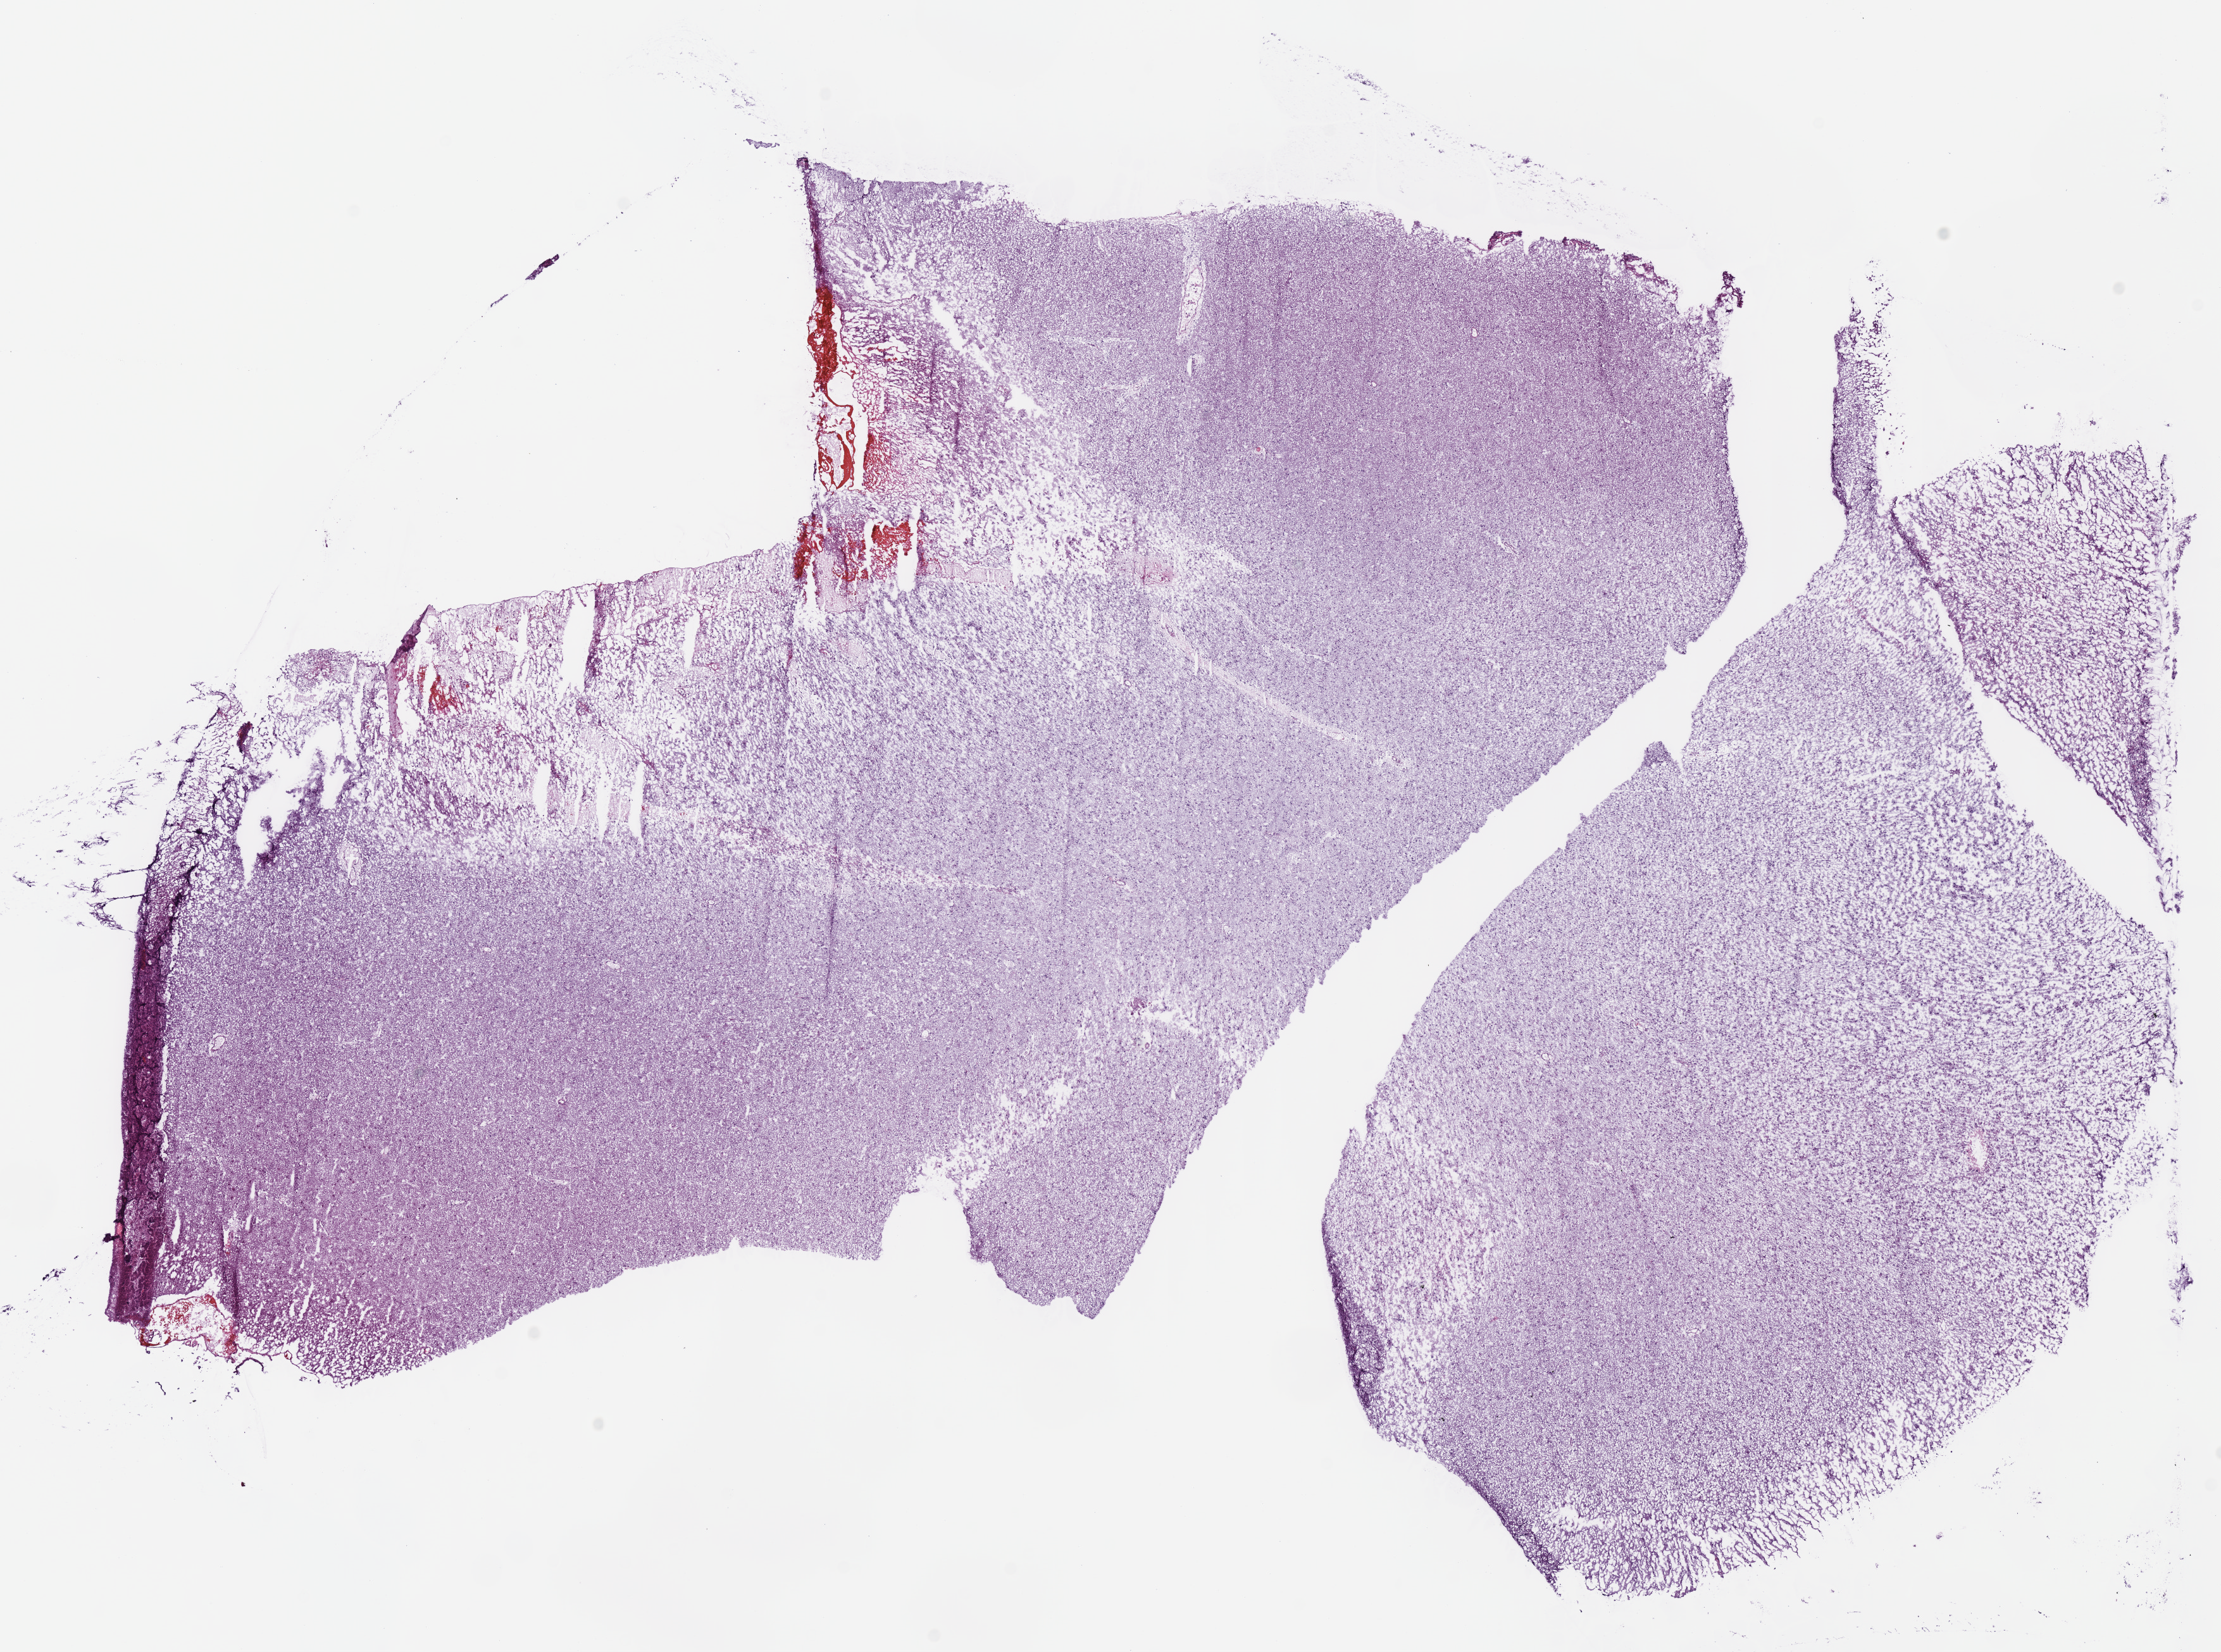
Digitized H&E-stained tissue section (whole slide) — a low-resolution overview of the entire scanned area, about 13.8 x 10.3 mm. Frozen section. Brain, primary tumour sample. Female patient; age at initial diagnosis 25 years. Histologic grade: G2 (moderately differentiated). Composition of this section per pathologist review: tumour cells 100%, tumour nuclei 65%, normal cells 0%, stromal cells 0%, necrosis 0%.
• diagnosis: Mixed glioma